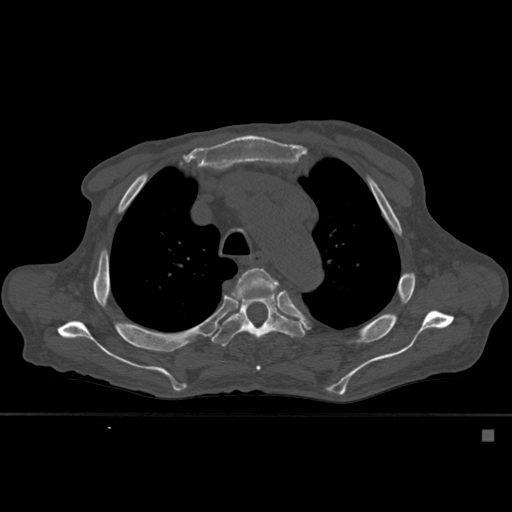
CT including the spine, one axial slice. Position 407 of 527 along the scan axis. Bone window (W 1800 / L 400 HU). 512 × 512 image matrix, field of view 373 × 373 mm. Male patient, age 78 years. Case-level facts recorded for this patient, not image findings: primary cancer: prostate.
Annotated regions visible in this slice (semi-automatic segmentation, software-assisted and operator-edited):
- T4 vertebra: bounding box <229,268,280,371> (left, top, right, bottom; pixels)
- T5 vertebra: <212,268,306,347>